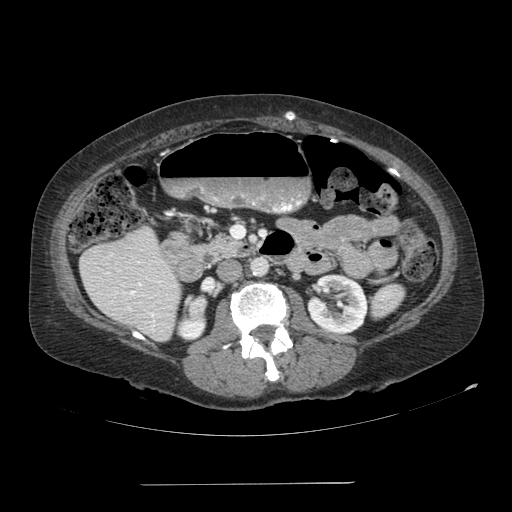
Contrast-enhanced abdominal CT, one axial slice. Slice 45 of 113 in the series (ordered by position). Reconstruction kernel SOFT. 120 kVp. Soft-tissue window (W 400 / L 40 HU). 2.5 mm slice thickness. 512 × 512 image matrix, field of view 440 × 440 mm. Female patient, age 67 years. From the clinical record (not read from this slice): diagnosis: adrenocortical carcinoma; tumour side: right adrenal; tumour size at pathology: 9.8 cm; Ki-67 index: 59 %; stage (as recorded): 4.
Annotated regions visible in this slice (semi-automatically segmented with operator editing):
- mass: bounding box [x1, y1, x2, y2] px = [190, 297, 205, 317]